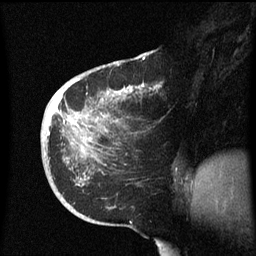
Breast MRI (dynamic contrast-enhanced), one sagittal slice. Position 25 of 60 along the scan axis. Dynamic contrast-enhanced series, image 2 of 3 at this slice position (ordered by acquisition). 1.5 T. TE 4.2 ms, TR 8.4 ms. 2.3 mm slice thickness. 256 × 256 image matrix. Patient: female, 38 years. Case-level facts recorded for this patient, not image findings: setting: breast cancer imaged before/during neoadjuvant chemotherapy; receptor status: HER2-positive.
Annotated regions visible in this slice (semi-automatic segmentation, software-assisted and operator-edited):
- analysis volume of interest (the breast-tissue region the enhancement analysis was run in; not a lesion): box from (x=41, y=78) to (x=161, y=213) px
- tumour enhancement mask (voxels above the 70 % enhancement threshold inside the analysis volume of interest): (x=48, y=84)–(x=159, y=135)